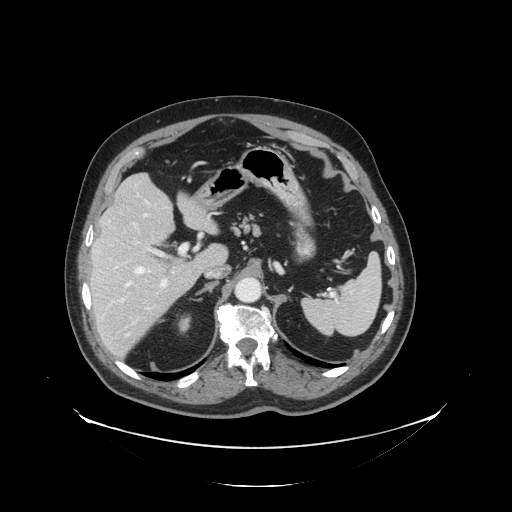
Contrast-enhanced abdominal CT, one axial slice; slice 89 of 138 in the series (ordered by position); 120 kVp; intravenous contrast given; soft-tissue window (W 400 / L 40 HU); 2.5 mm slice thickness; 512 × 512 image matrix. Male patient, age 77 years. From the clinical record (not read from this slice): diagnosis: colorectal cancer liver metastases, imaged before liver resection; multiple liver metastases: no; largest metastasis: 1.5 cm; disease in both lobes: no.
Outlined on this slice (outlined manually by an expert reader):
- hepatic veins: bounding box (x1, y1, x2, y2) in pixels: (125, 214, 147, 335)
- liver: (91, 174, 227, 357)
- planned liver remnant (the part of the liver to remain after resection): (92, 174, 224, 288)
- portal vein (with intrahepatic branches): (116, 234, 203, 303)